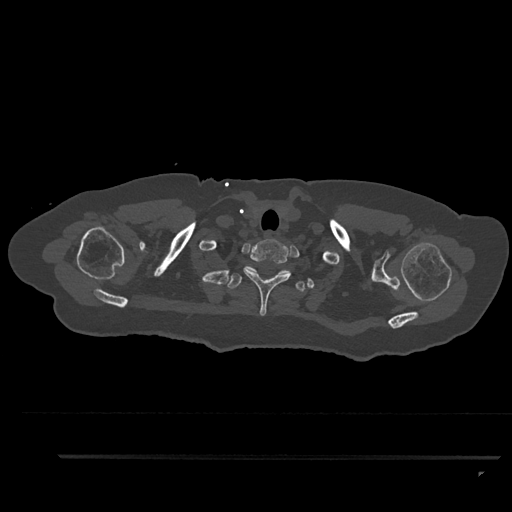
CT including the spine, one axial slice; slice 751 of 797 in the series (ordered by position); reconstruction kernel Br40s/3; 120 kVp; bone window (W 1800 / L 400 HU); 0.5 mm slice thickness; 512 × 512 image matrix. Patient: female, 44 years. Case-level facts recorded for this patient, not image findings: primary cancer: renal; vertebrae with lytic lesions (as recorded): L1.
Structures marked on this image (semi-automatic segmentation, software-assisted and operator-edited):
- T1 vertebra: bounding box <241,239,291,316> (left, top, right, bottom; pixels)
- T2 vertebra: <227,273,306,292>